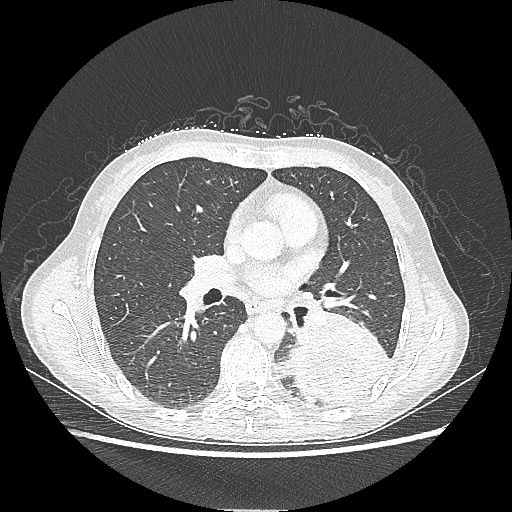
Chest CT, one axial slice; position 118 of 220 along the scan axis; reconstruction kernel LUNG; lung window (W 1500 / L -600 HU); 1.25 mm slice thickness; 512 × 512 image matrix. Patient: female, 53 years. Case-level facts recorded for this patient, not image findings: clinical TNM (as recorded): T3 N0 M0.
Annotated regions visible in this slice (rectangle marked by the reading radiologist):
- lung tumour (recorded histology: adenocarcinoma): box from (x=289, y=315) to (x=390, y=406) px